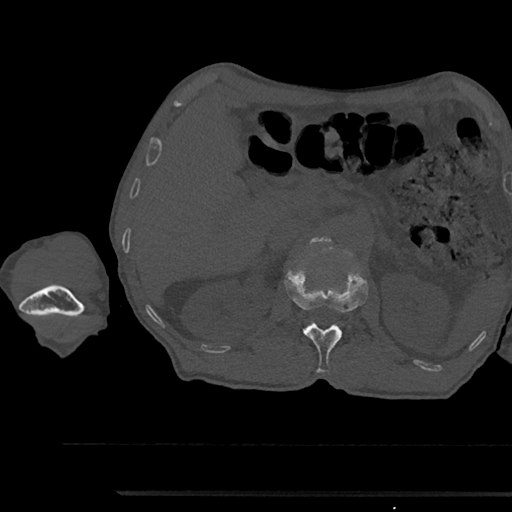
CT including the spine, one axial slice; position 625 of 797 along the scan axis; reconstruction kernel Br40s/3; 120 kVp; bone window (W 1800 / L 400 HU); 0.5 mm slice thickness; 512 × 512 image matrix. Male patient, age 79 years. From the clinical record (not read from this slice): primary cancer: prostate.
Outlined on this slice (semi-automatically segmented with operator editing):
- L1 vertebra: bounding box [x1, y1, x2, y2] px = [285, 270, 368, 373]
- L2 vertebra: [309, 237, 328, 243]